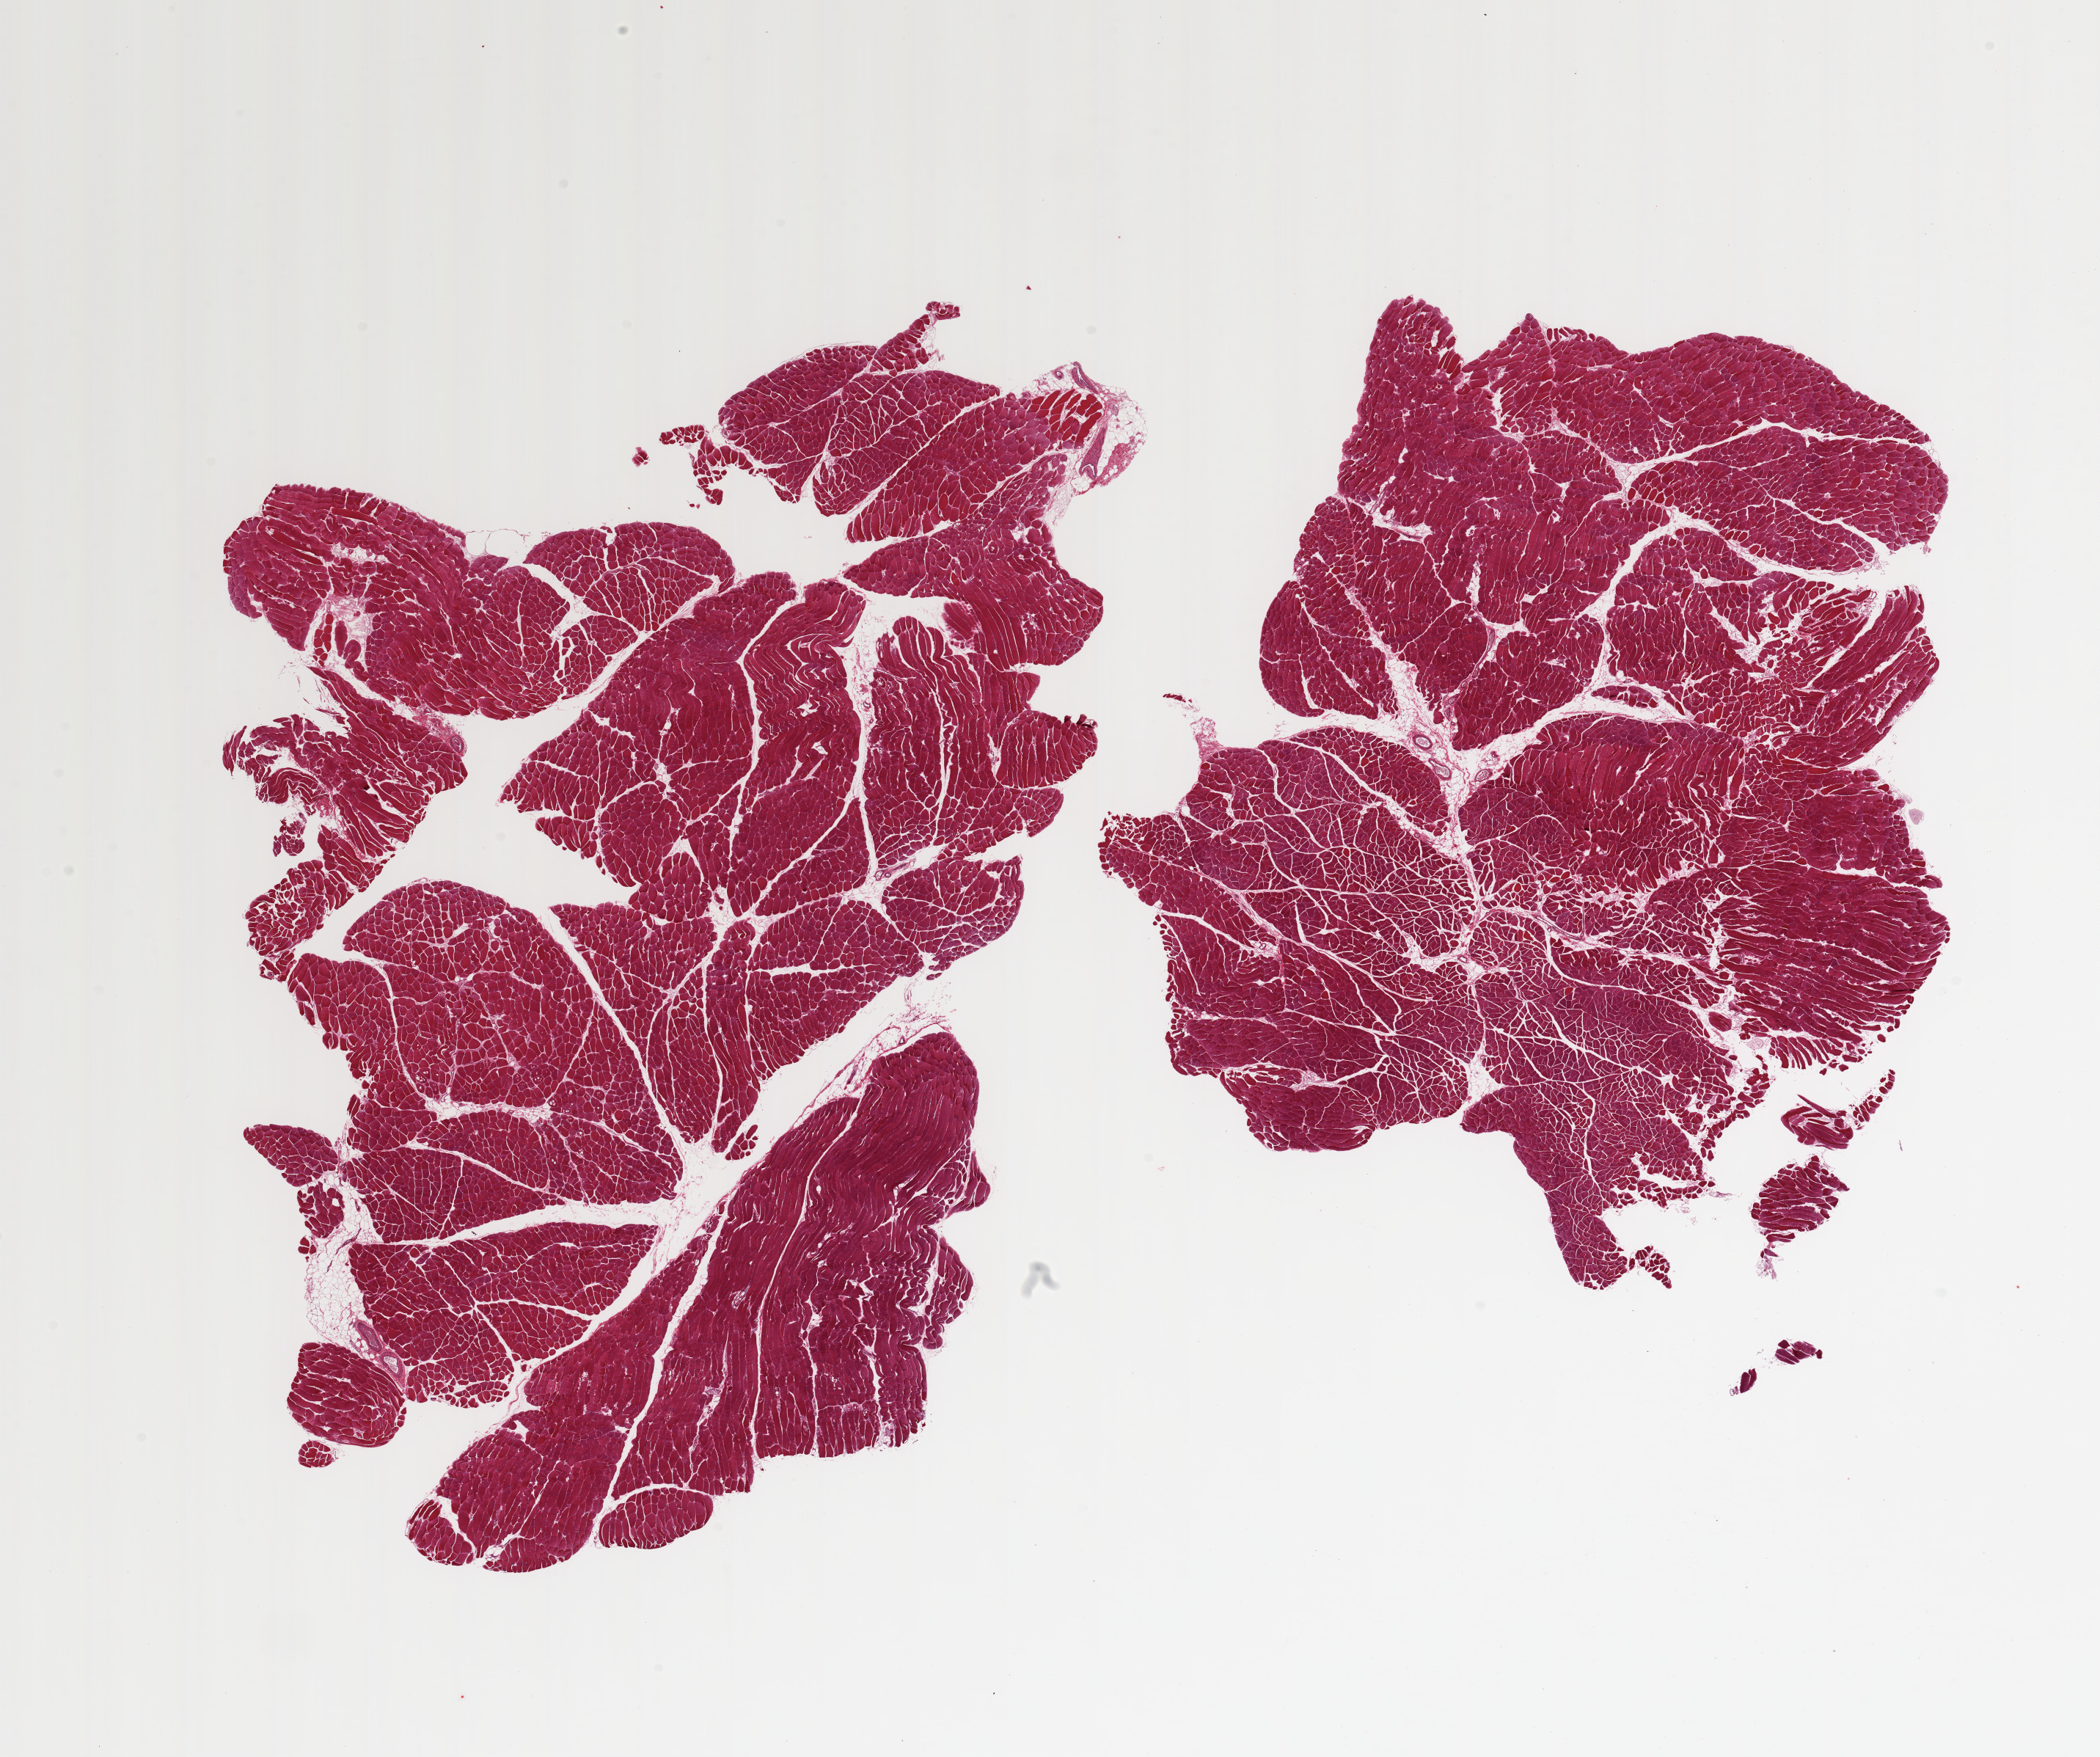
Digitized H&E-stained section, shown as a low-resolution overview of the whole scanned area (about 22.6 x 18.9 mm, slide scanned at 20x); PAXgene-fixed paraffin-embedded (PFPE) section; target tissue: skeletal muscle; donor tissue sample. Male donor.
- reviewer comment on this tissue sample: 2 pieces;10% internal fat